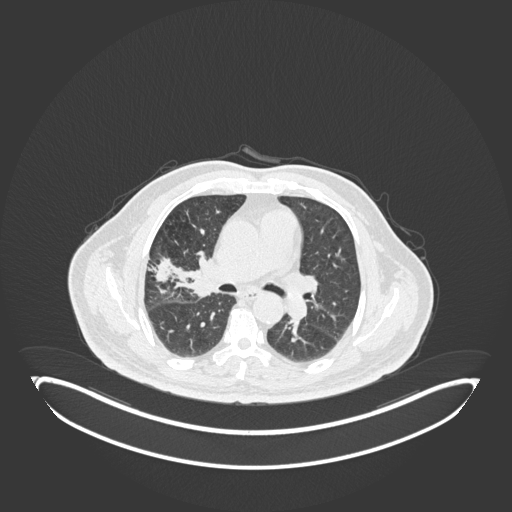
Chest CT, one axial slice. Position 99 of 247 along the scan axis. 120 kVp. Lung window (W 1500 / L -600 HU). 1 mm slice thickness. 512 × 512 image matrix, field of view 500 × 500 mm. Male patient, age 72 years. Case-level facts recorded for this patient, not image findings: clinical TNM (as recorded): T1c N0 M0; histopathological grade: G2.
Outlined on this slice (rectangle marked by the reading radiologist):
- lung tumour (recorded histology: squamous cell carcinoma): bounding box (x1, y1, x2, y2) in pixels: (182, 254, 212, 300)